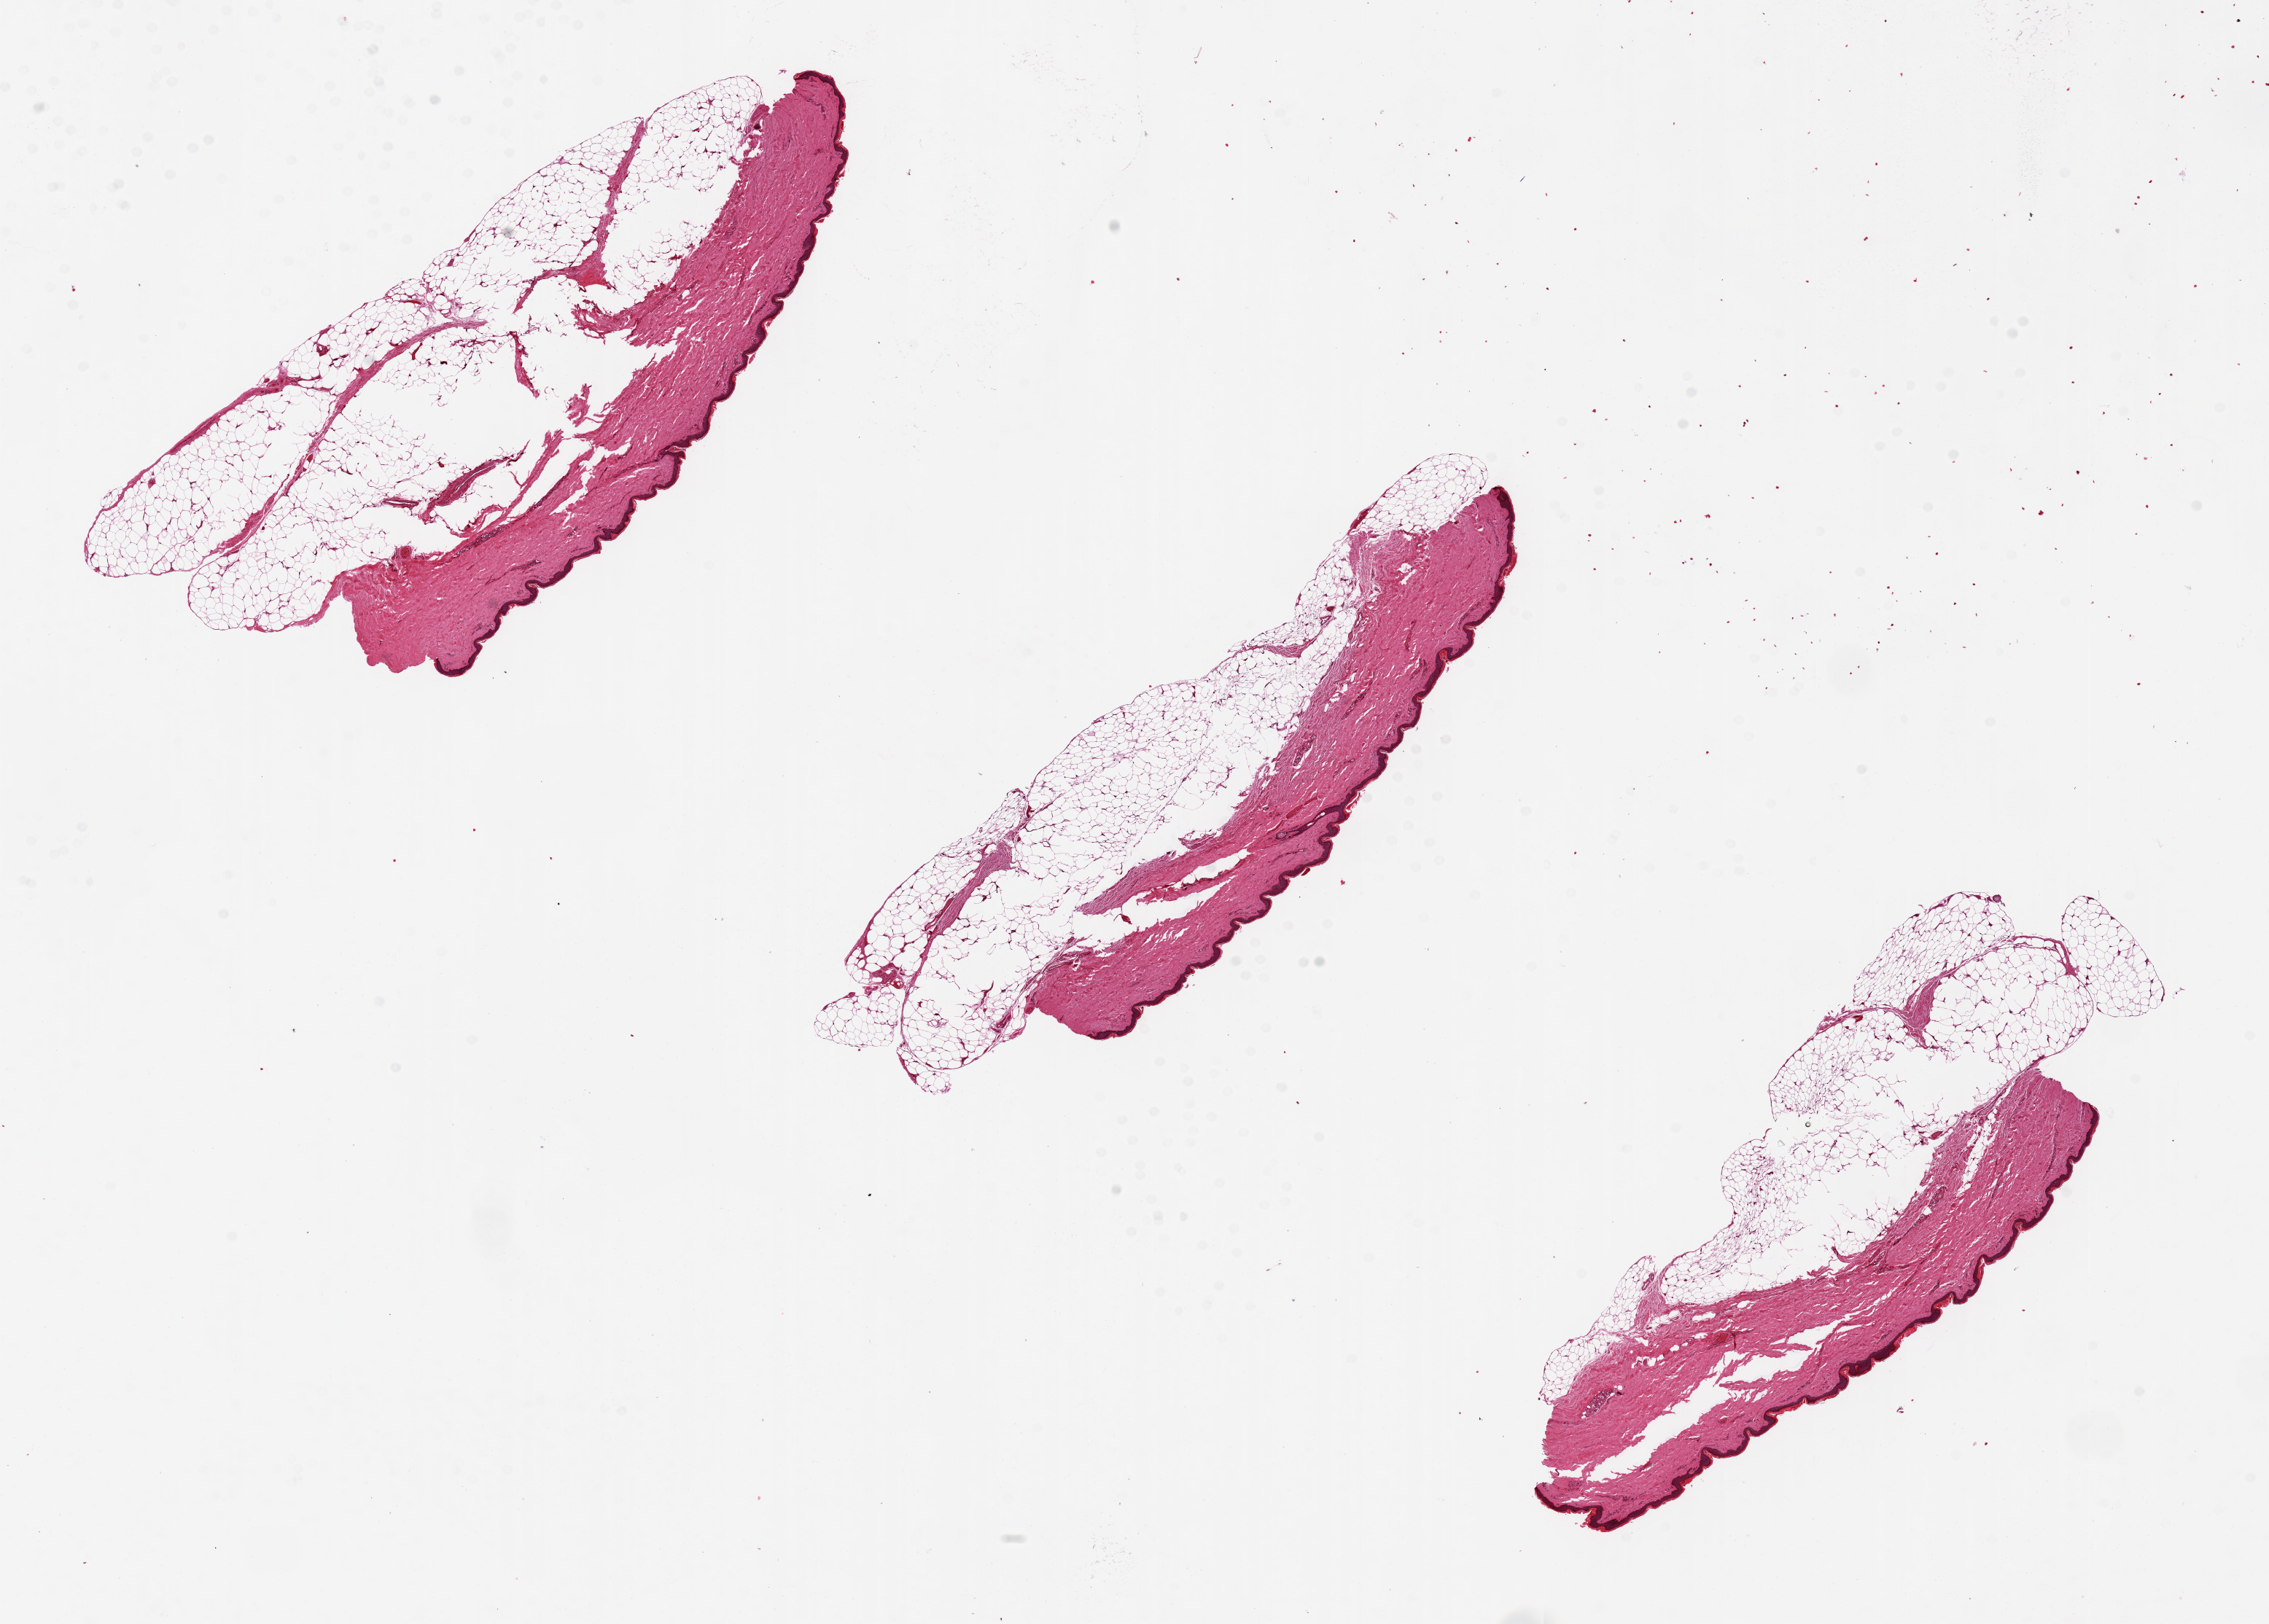
H&E whole-slide image, brightfield — whole scanned area (about 24.6 x 17.6 mm, acquisition: 20x scan) shown as a low-resolution overview, PAXgene-fixed, paraffin-embedded tissue, sampled site (target tissue): skin of lower leg, tissue donor sample.
Review note (as recorded): 3 pieces. Few appendages.